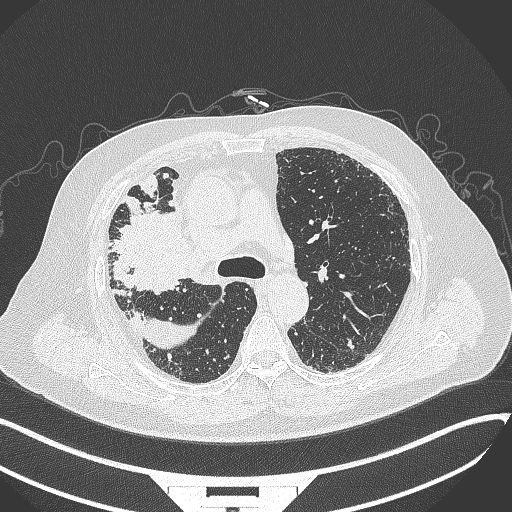
Chest CT, one axial slice. Position 230 of 384 along the scan axis. Reconstruction kernel B70f. 120 kVp. Lung window (W 1500 / L -600 HU). 1 mm slice thickness. 512 × 512 image matrix, field of view 400 × 400 mm. Patient: male, 69 years. From the clinical record (not read from this slice): clinical TNM (as recorded): T4 N3 M1.
Structures marked on this image (bounding box drawn by a radiologist):
- lung tumour (recorded histology: adenocarcinoma): bounding box <113,208,195,301> (left, top, right, bottom; pixels)